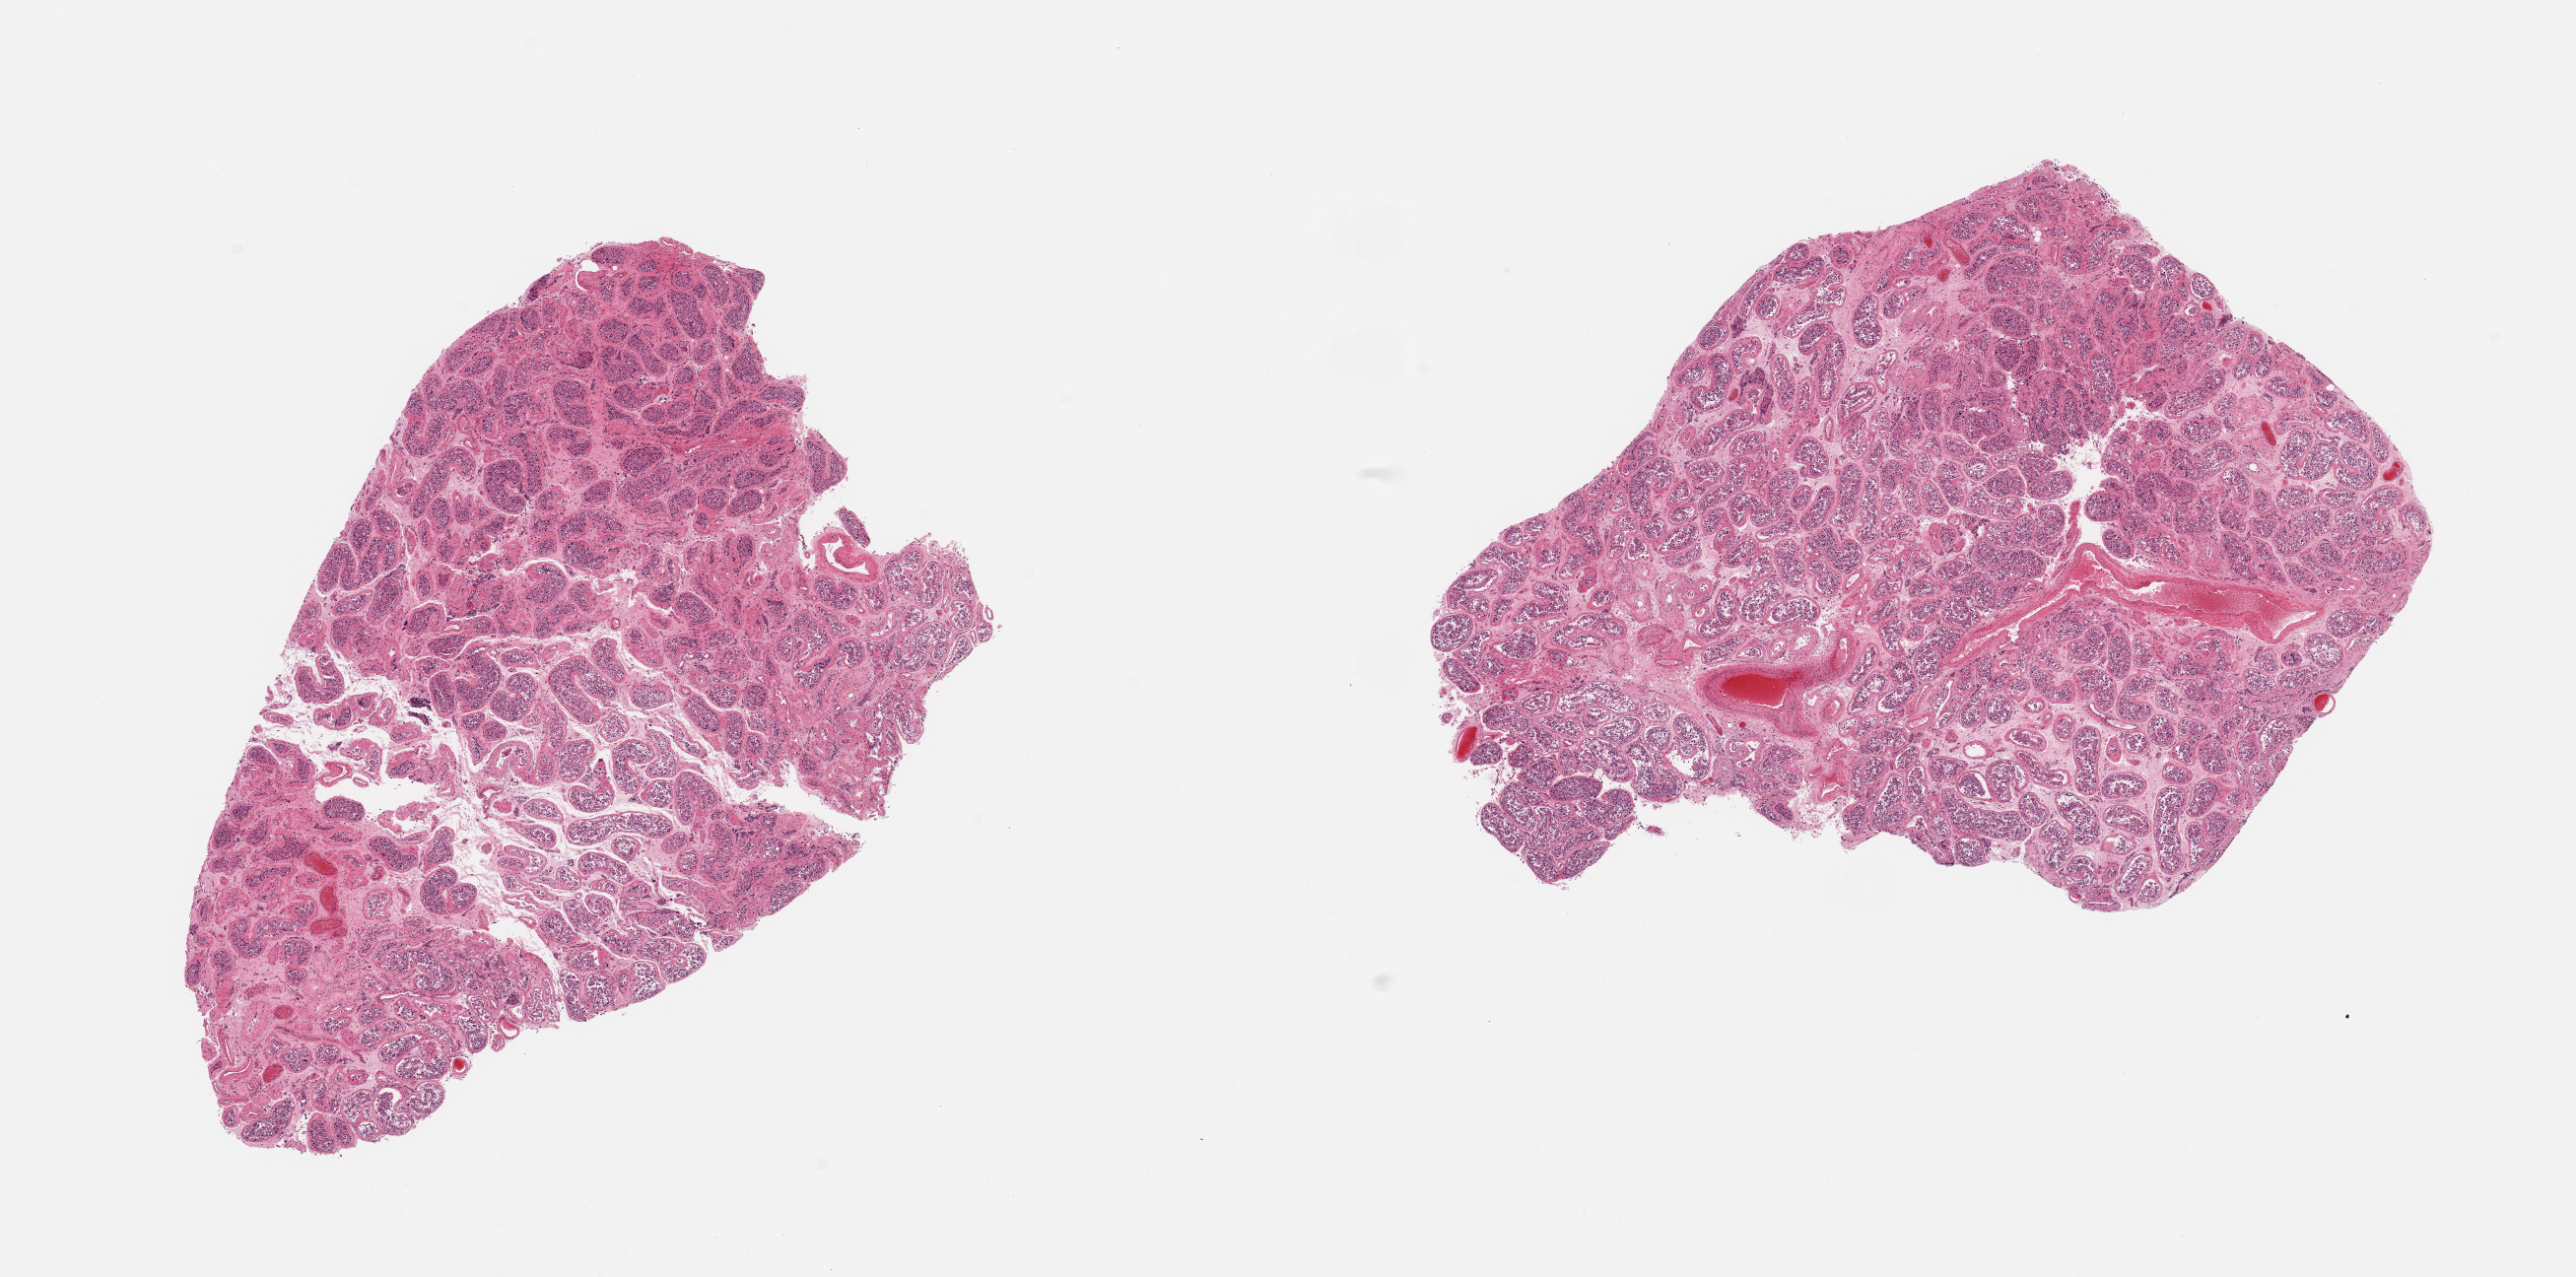
Hematoxylin and eosin (H&E) whole-slide image, a low-resolution overview of the entire scanned area, about 20.7 x 10.2 mm (slide scanned at 20x), PAXgene-fixed, paraffin-embedded tissue, section of testis (target tissue), tissue donor sample. Donor sex: male.
Review note (as recorded): 2 pieces; some peritubular fibrosis and hyalinization.